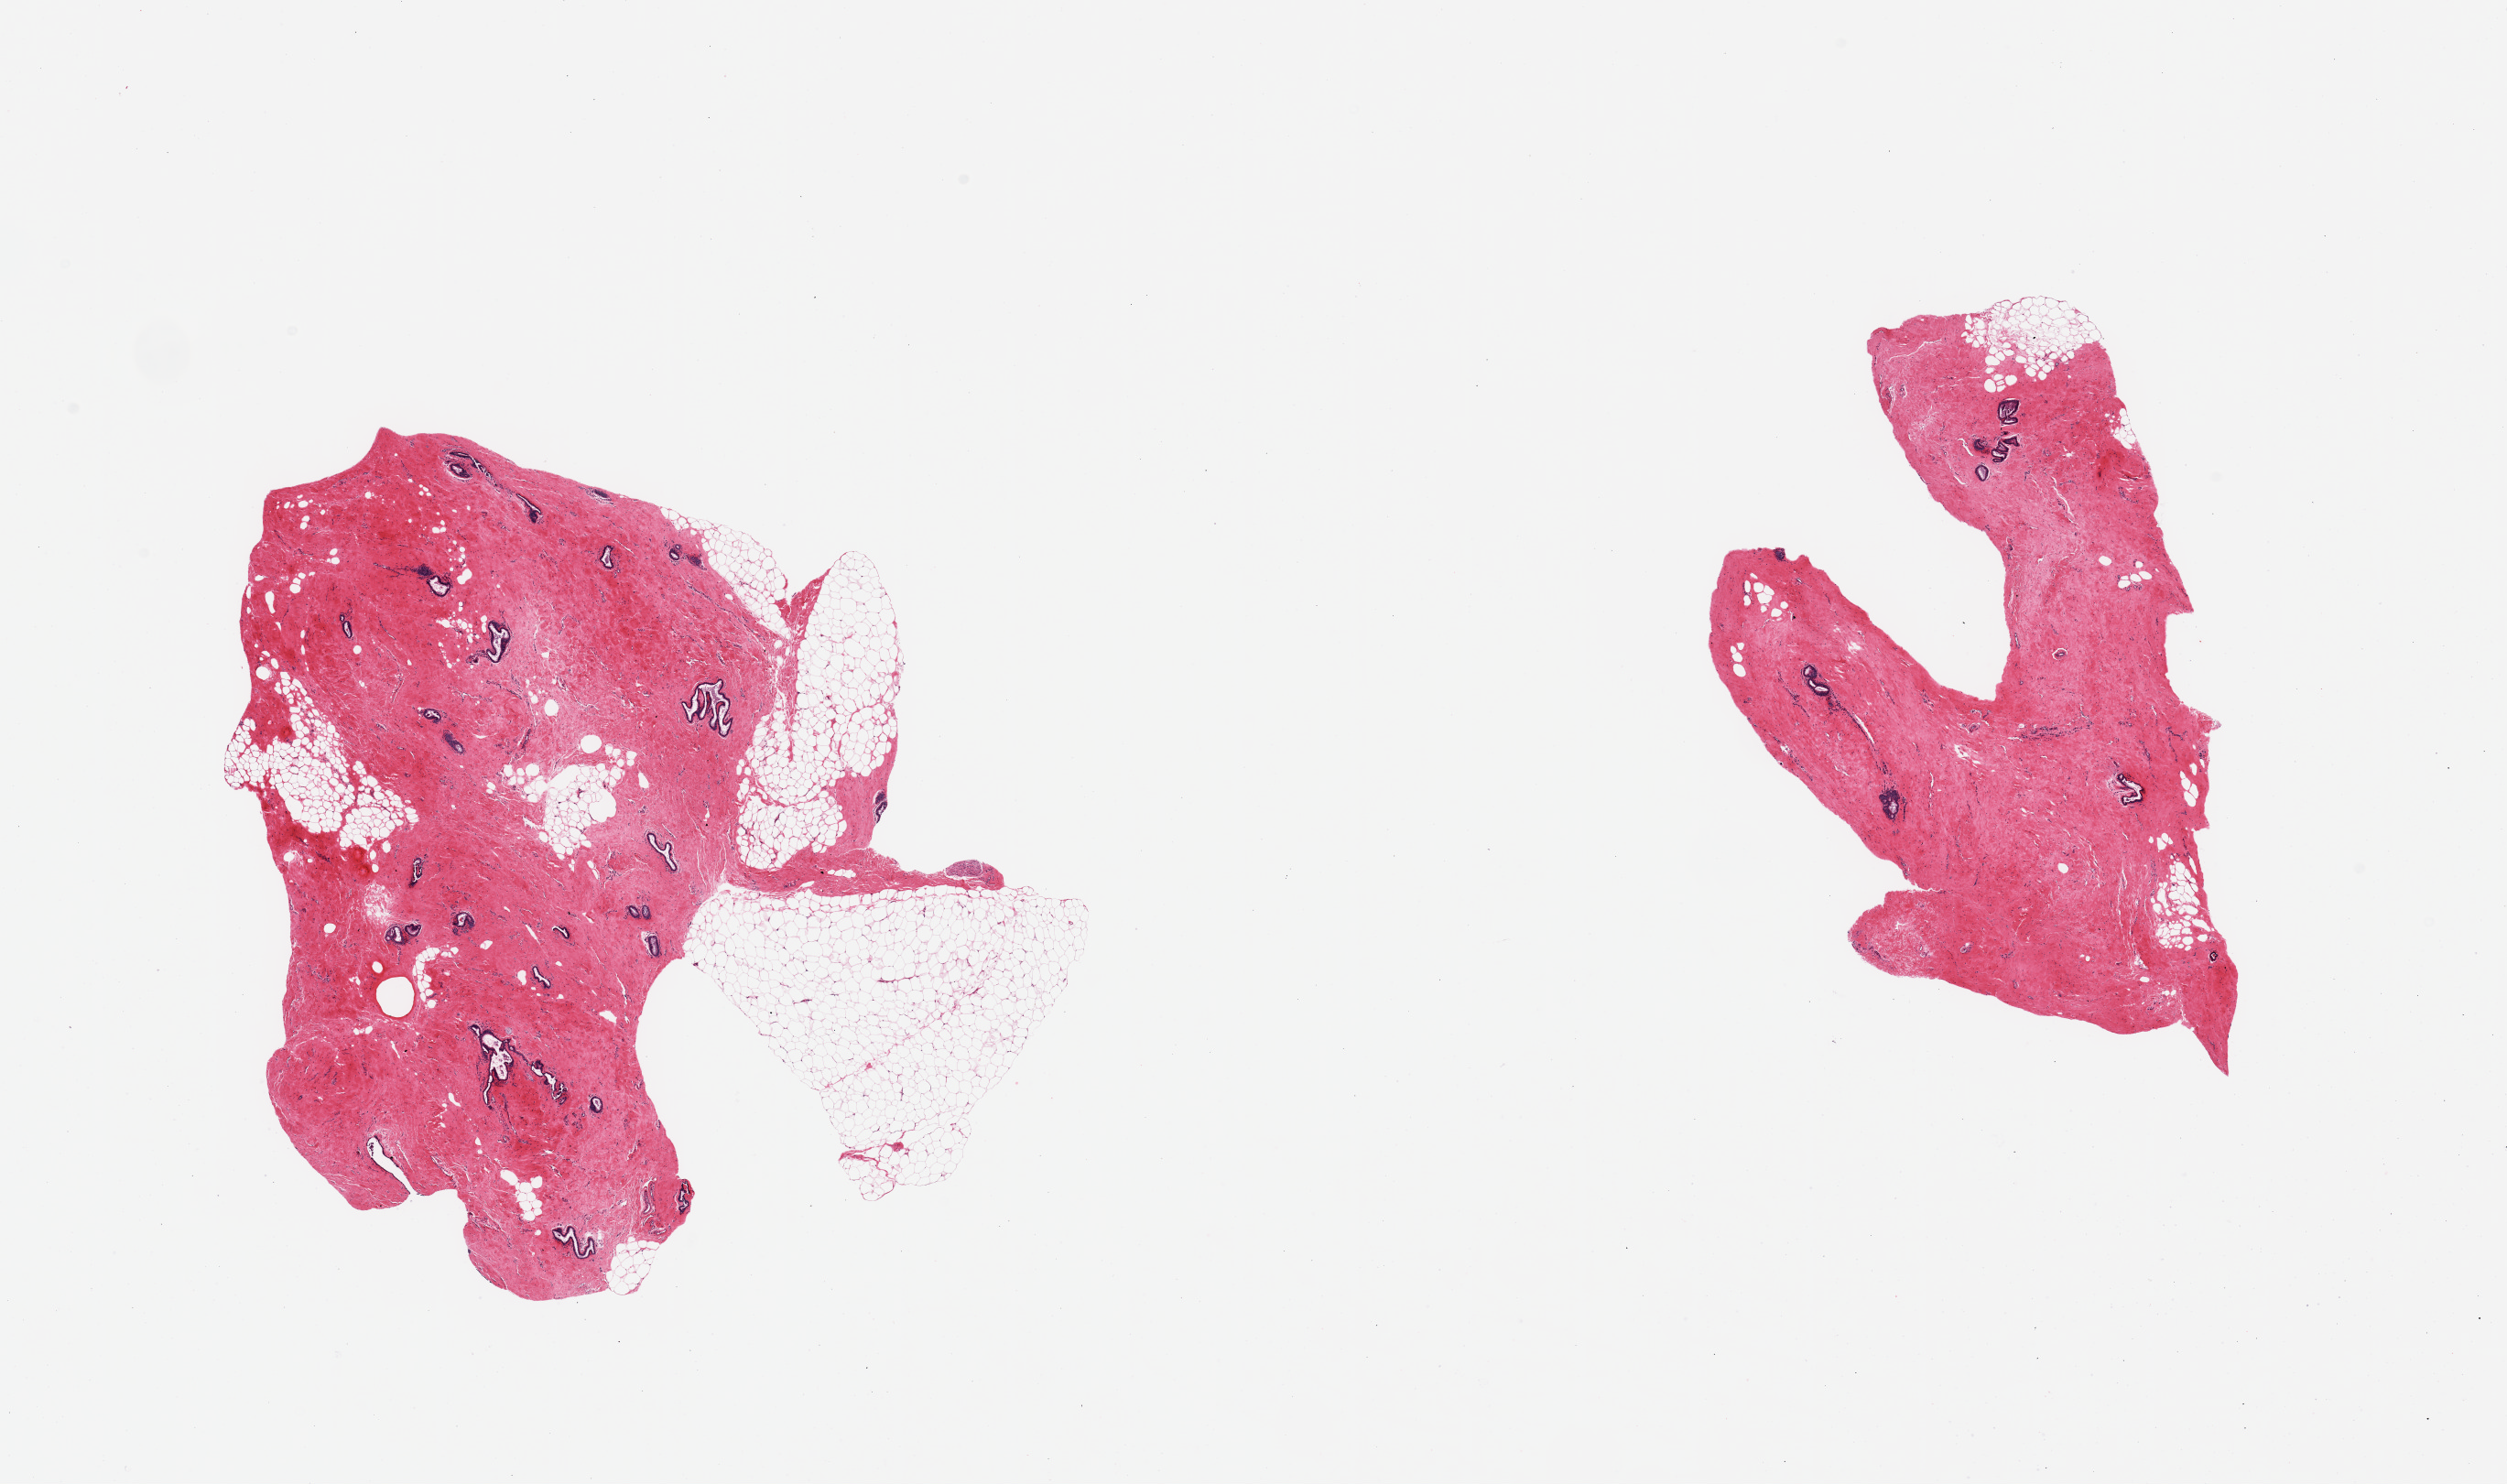
Whole-slide image, haematoxylin and eosin stain — whole scanned area (about 21.7 x 12.8 mm) shown as a low-resolution overview. PAXgene-fixed paraffin-embedded (PFPE) section. Section of breast (target tissue). Tissue donor sample. Male donor.
- review note (as recorded): 2 pieces, gynecomastoid stromal and ductal hyperplasia